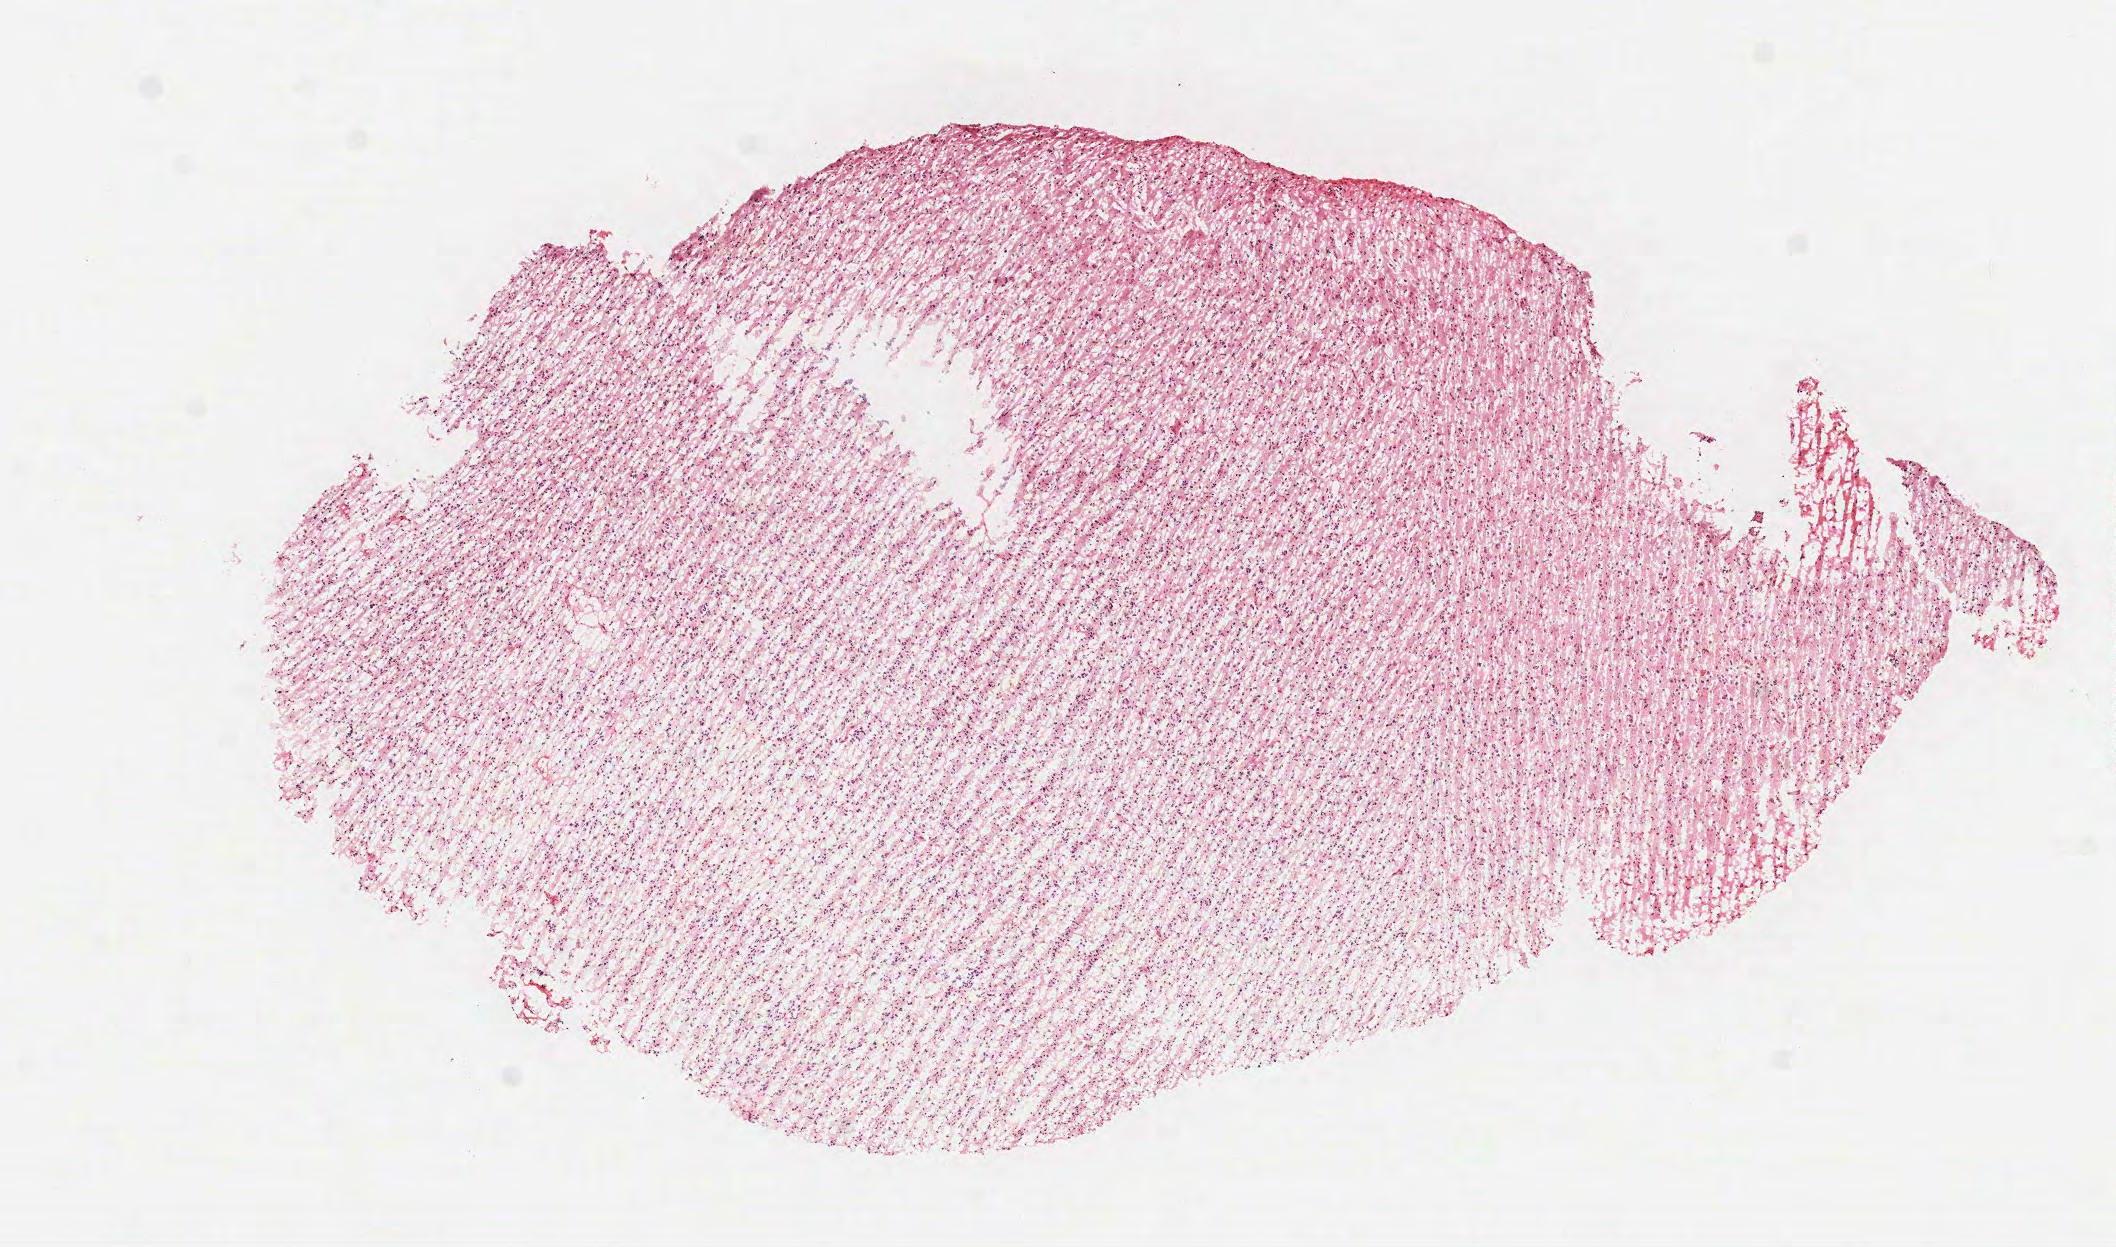
Whole-slide histology image, H&E-stained — whole scanned area (about 8.5 x 5.0 mm) shown as a low-resolution overview, frozen section from the top of the tissue portion, recurrent tumour sample from the brain. Female patient; age at initial diagnosis 48 years. Slide review estimates, as recorded: tumour cells 100%, tumour nuclei 65%, normal cells 0%, stromal cells 0%, necrosis 0%.
* this section: recurrent tumour
* patient diagnosis: Glioblastoma